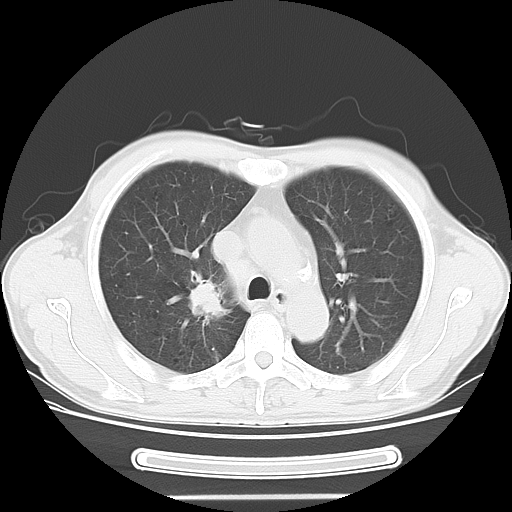
Chest CT, one axial slice; slice 35 of 51 in the series (ordered by position); reconstruction kernel LUNG; 120 kVp; lung window (W 1500 / L -600 HU); 5 mm slice thickness; 512 × 512 image matrix, field of view 350 × 350 mm. Male patient, age 57 years. Case-level facts recorded for this patient, not image findings: clinical TNM (as recorded): T2 N3 M1b.
Annotated regions visible in this slice (rectangle marked by the reading radiologist):
- lung tumour (recorded histology: adenocarcinoma): box from (x=183, y=277) to (x=231, y=324) px